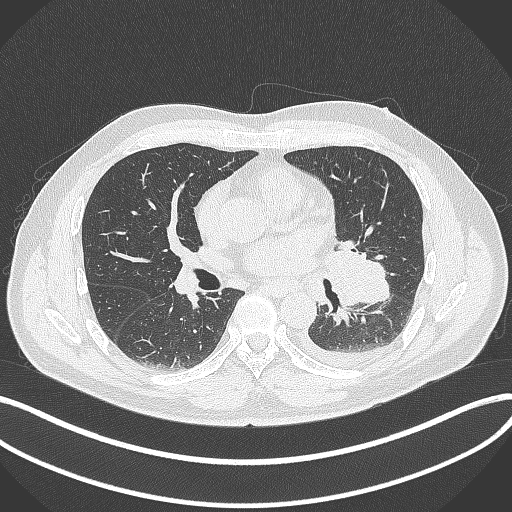
Chest CT, one axial slice. Slice 186 of 342 in the series (ordered by position). Reconstruction kernel B70f. Lung window (W 1500 / L -600 HU). 1 mm slice thickness. 512 × 512 image matrix, field of view 400 × 400 mm. Male patient, age 58 years. From the clinical record (not read from this slice): clinical TNM (as recorded): T3 N1 M1b.
Annotated regions visible in this slice (bounding box drawn by a radiologist):
- lung tumour (recorded histology: small cell carcinoma): bounding box [x1, y1, x2, y2] px = [323, 233, 391, 314]